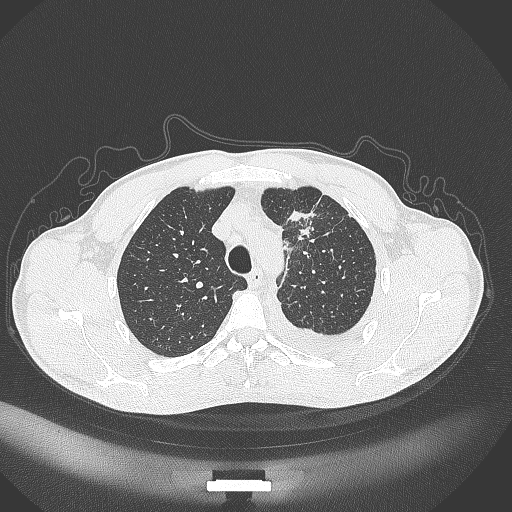
Chest CT, one axial slice. Slice 269 of 371 in the series (ordered by position). 120 kVp. Lung window (W 1500 / L -600 HU). 512 × 512 image matrix. Male patient, age 49 years. From the clinical record (not read from this slice): clinical TNM (as recorded): T1c N1 M1.
Structures marked on this image (rectangle marked by the reading radiologist):
- lung tumour (recorded histology: adenocarcinoma): box from (x=283, y=209) to (x=322, y=247) px